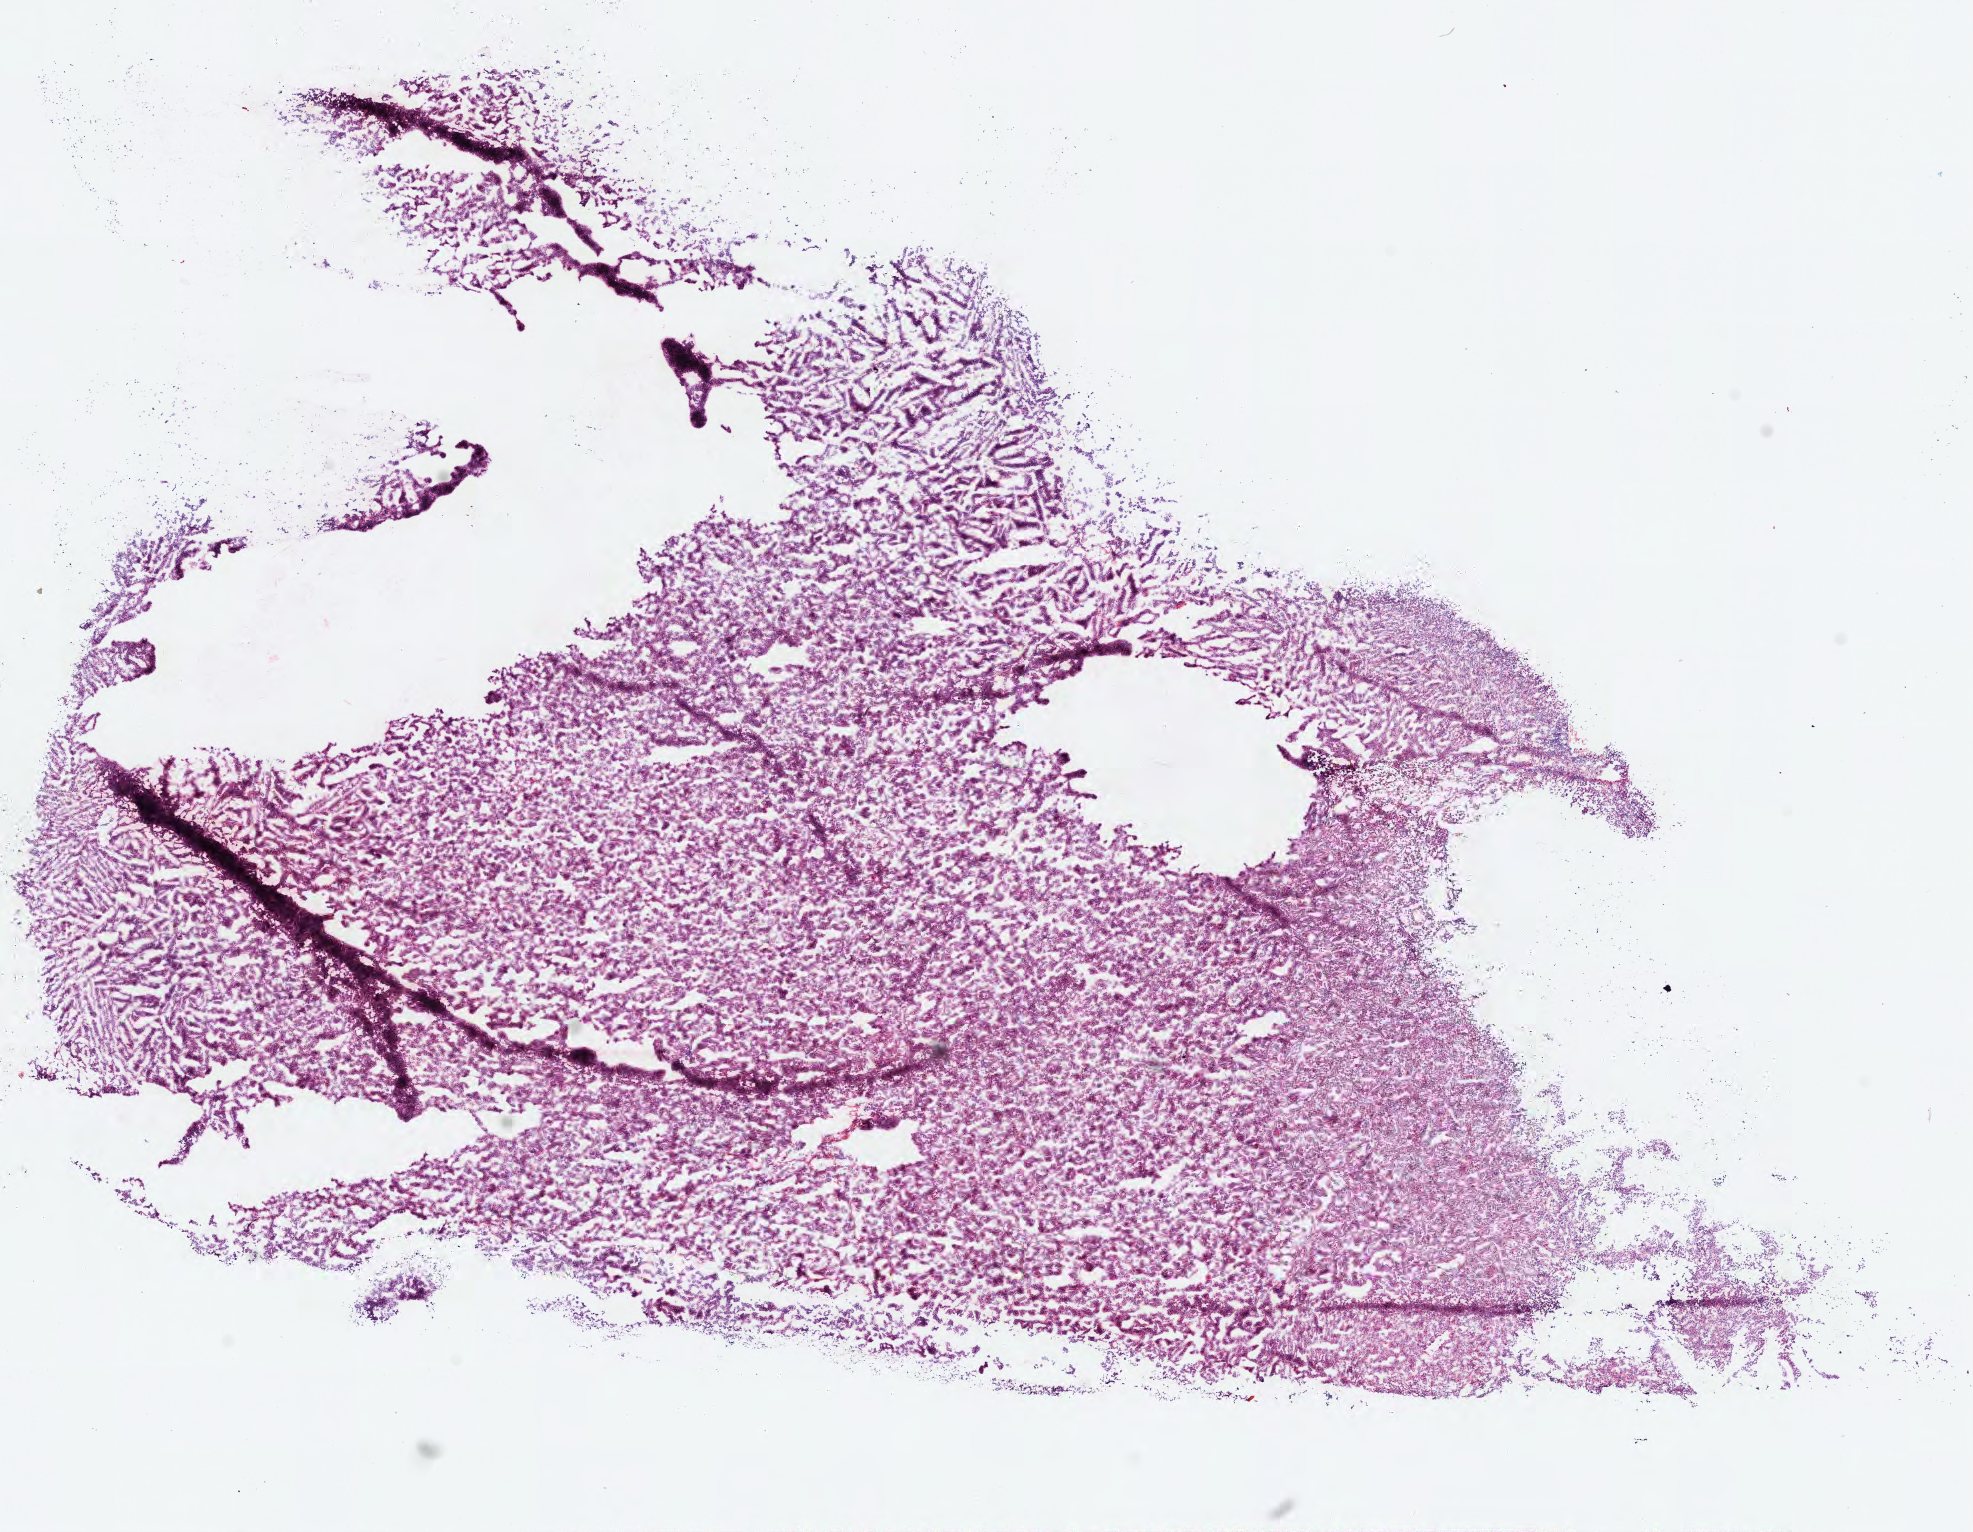
Digitized H&E-stained tissue section (whole slide), a low-resolution overview of the entire scanned area, about 14.7 x 11.4 mm (slide scanned at 20x), FFPE section, primary tumour sample from the lymphoid tissue. Male, age 36 years at initial diagnosis.
Pathologic diagnosis: Diffuse large B-cell lymphoma, NOS (lymph nodes of head, face and neck).